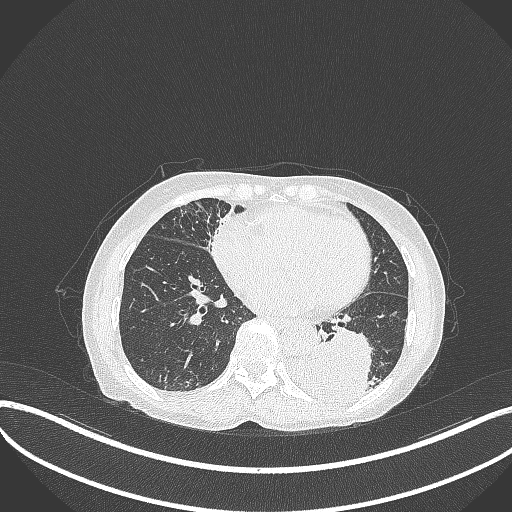
Chest CT, one axial slice. Slice 110 of 370 in the series (ordered by position). Reconstruction kernel B70f. Lung window (W 1500 / L -600 HU). 512 × 512 image matrix, field of view 400 × 400 mm. Female patient, age 78 years. From the clinical record (not read from this slice): clinical TNM (as recorded): T3 N0 M1.
Annotated regions visible in this slice (rectangle marked by the reading radiologist):
- lung tumour (recorded histology: squamous cell carcinoma): bounding box [x1, y1, x2, y2] px = [281, 324, 376, 406]